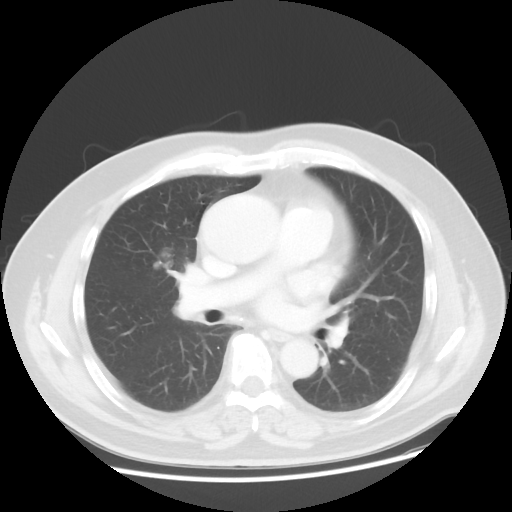
Chest CT, one axial slice; reconstruction kernel STANDARD; lung window (W 1500 / L -600 HU); 512 × 512 image matrix, field of view 392 × 392 mm. Patient: male, 60 years. From the clinical record (not read from this slice): clinical TNM (as recorded): T2 N3 M0; histopathological grade: G2-3.
Annotated regions visible in this slice (rectangle marked by the reading radiologist):
- lung tumour (recorded histology: adenocarcinoma): bounding box (x1, y1, x2, y2) in pixels: (145, 244, 188, 287)